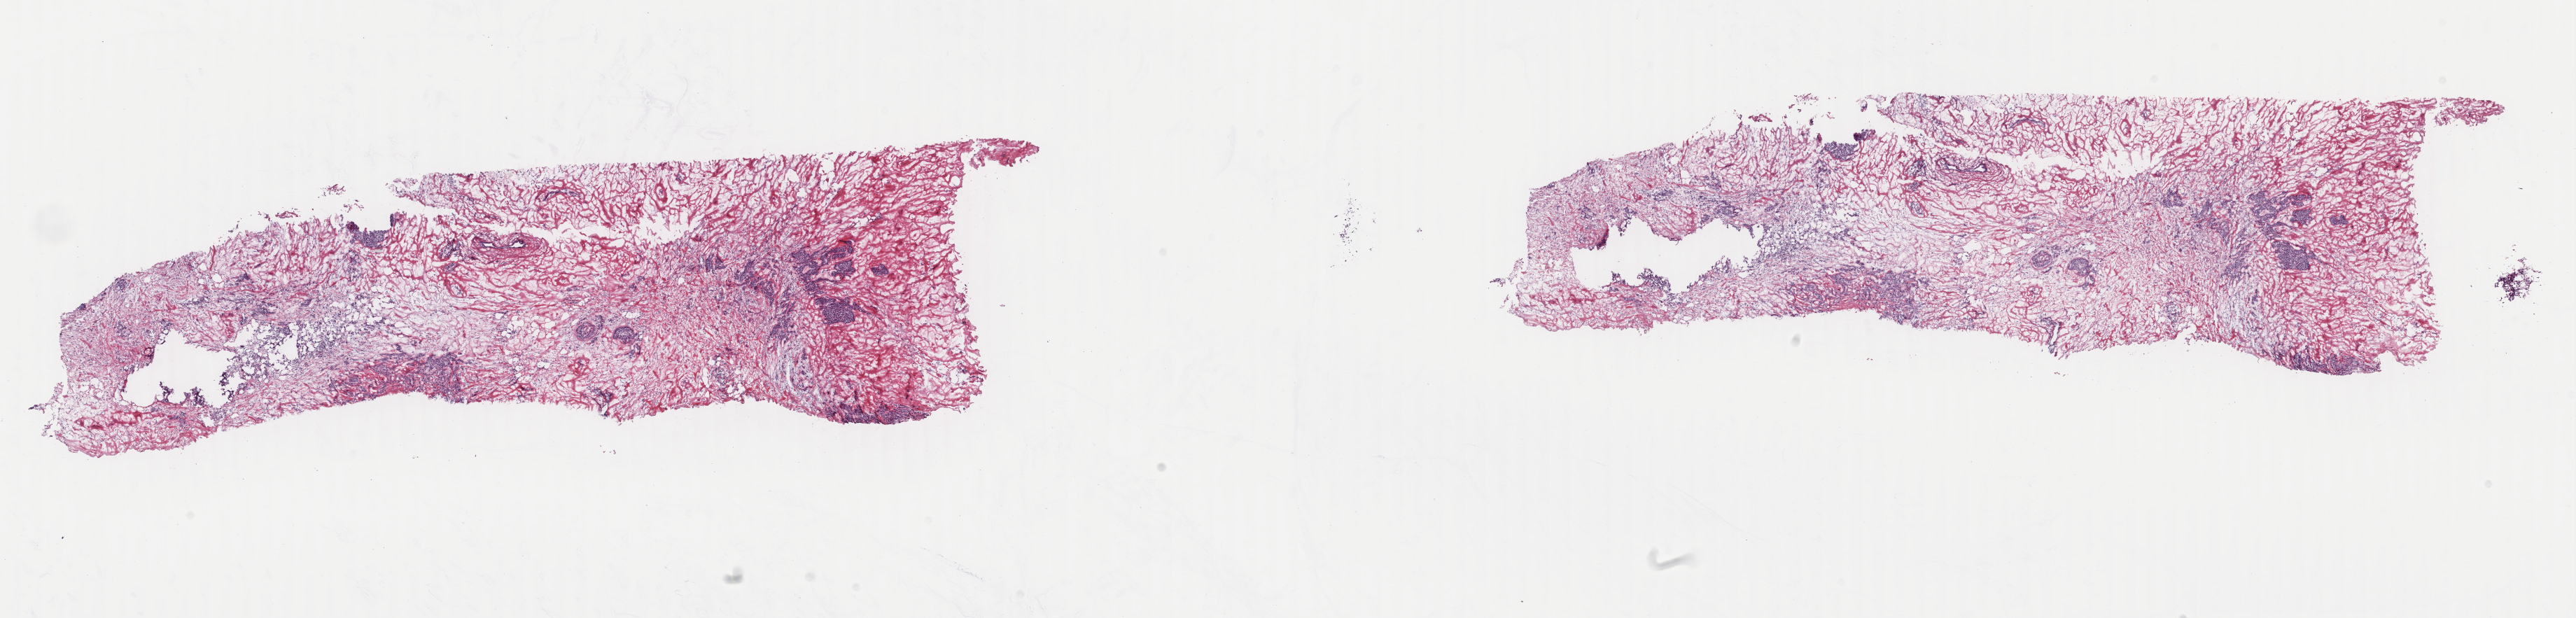
Digitized Hematoxylin and eosin (H&E) stained tissue section (whole slide), low-resolution overview of the scanned area, about 29.3 x 7.0 mm (from a 40x scan); frozen section; sample: primary tumour, breast. Female patient; age at initial diagnosis 62 years.
Diagnosis: Infiltrating lobular mixed with other types of carcinoma.